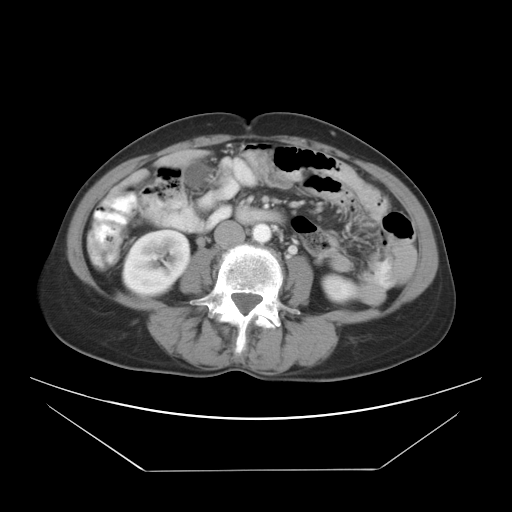
Contrast-enhanced abdominal CT, one axial slice. Reconstruction kernel STANDARD. 120 kVp. Soft-tissue window (W 400 / L 40 HU). 7.5 mm slice thickness. 512 × 512 image matrix, field of view 412 × 412 mm. Female patient, age 54 years. Case-level facts recorded for this patient, not image findings: diagnosis: colorectal cancer liver metastases, imaged before liver resection; multiple liver metastases: yes; largest metastasis: 2.5 cm.
Structures marked on this image (outlined manually by an expert reader):
- liver: bounding box <178,156,185,157> (left, top, right, bottom; pixels)
- planned liver remnant (the part of the liver to remain after resection): <179,157,181,159>